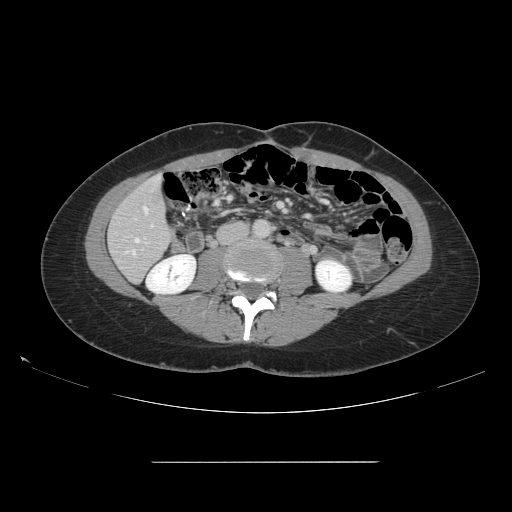
Contrast-enhanced abdominal CT, one axial slice. Position 38 of 151 along the scan axis. 120 kVp. Intravenous contrast given. Soft-tissue window (W 400 / L 40 HU). 2.5 mm slice thickness. 512 × 512 image matrix, field of view 421 × 421 mm. Female patient, age 46 years. From the clinical record (not read from this slice): diagnosis: colorectal cancer liver metastases, imaged before liver resection; multiple liver metastases: yes; largest metastasis: 3 cm; chemotherapy before resection: no.
Outlined on this slice (outlined manually by an expert reader):
- hepatic veins: bounding box (x1, y1, x2, y2) in pixels: (135, 207, 148, 242)
- liver: (110, 178, 172, 282)
- planned liver remnant (the part of the liver to remain after resection): (110, 177, 172, 281)